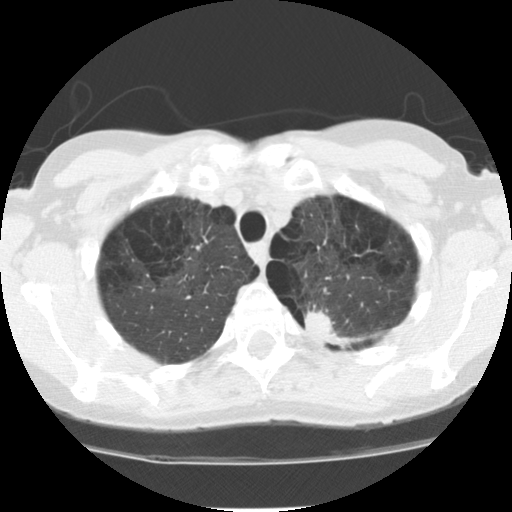
Low-dose screening chest CT, axial slice. Baseline screening round. Lung window (W 1500 / L -600 HU). 2.5 mm slice thickness. Standard (soft-tissue) reconstruction kernel (STANDARD). 512 × 512 image matrix, field of view 300 × 300 mm. Female participant, aged 61 years at enrolment. Current smoker at enrolment.
Lesion marked by an expert reader, bounding box (x1, y1, x2, y2) in pixels: (291, 298, 348, 351). The screening reader recorded 4 non-calcified nodules or masses ≥4 mm on this exam (left upper lobe, right lower lobe, right middle lobe, left lower lobe); which of them this box marks is not recorded. Later outcome: lung cancer diagnosed 68 days after this screen — adenocarcinoma, NOS, left upper lobe, poorly differentiated (G3), stage IB (AJCC 6th edition), 17 mm at pathology.